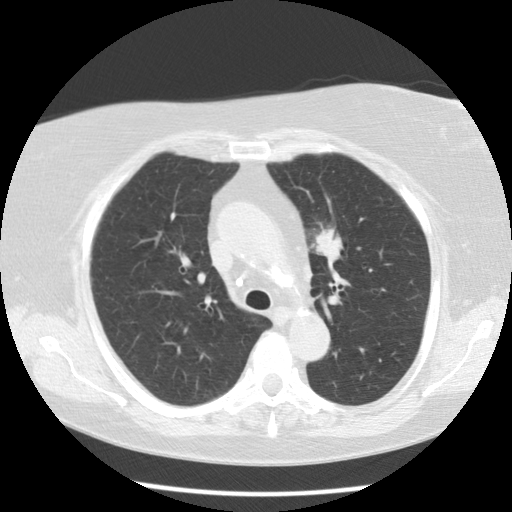
Low-dose screening chest CT, one axial slice; slice 80 of 109 in the series (ordered by position); 120 kVp; lung window (W 1500 / L -600 HU); 2.5 mm slice thickness; 512 × 512 image matrix, field of view 334 × 334 mm.
Annotated regions visible in this slice (manually delineated by an expert):
- lesion 1 (tumor, upper lobe of left lung): bounding box <311,227,343,263> (left, top, right, bottom; pixels)